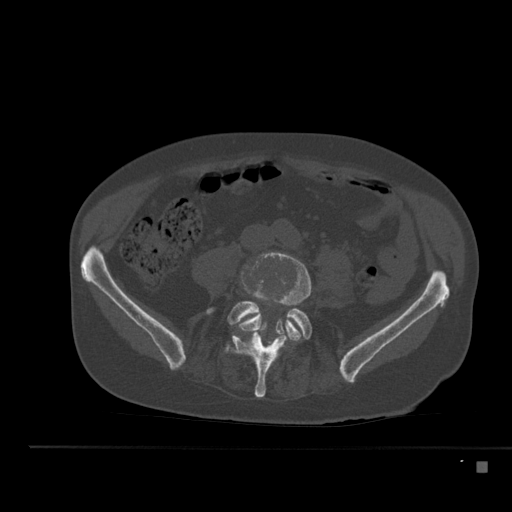
CT including the spine, one axial slice; position 133 of 517 along the scan axis; reconstruction kernel Br40s; bone window (W 1800 / L 400 HU); 1.5 mm slice thickness; 512 × 512 image matrix. Male patient, age 70 years. From the clinical record (not read from this slice): primary cancer: renal; vertebrae with lytic lesions (as recorded): T4, T6, T10, T12, L3, L4, L5.
Annotated regions visible in this slice (semi-automatic segmentation, software-assisted and operator-edited):
- L4 vertebra: bounding box [x1, y1, x2, y2] px = [238, 252, 311, 341]
- L5 vertebra: [227, 301, 312, 398]